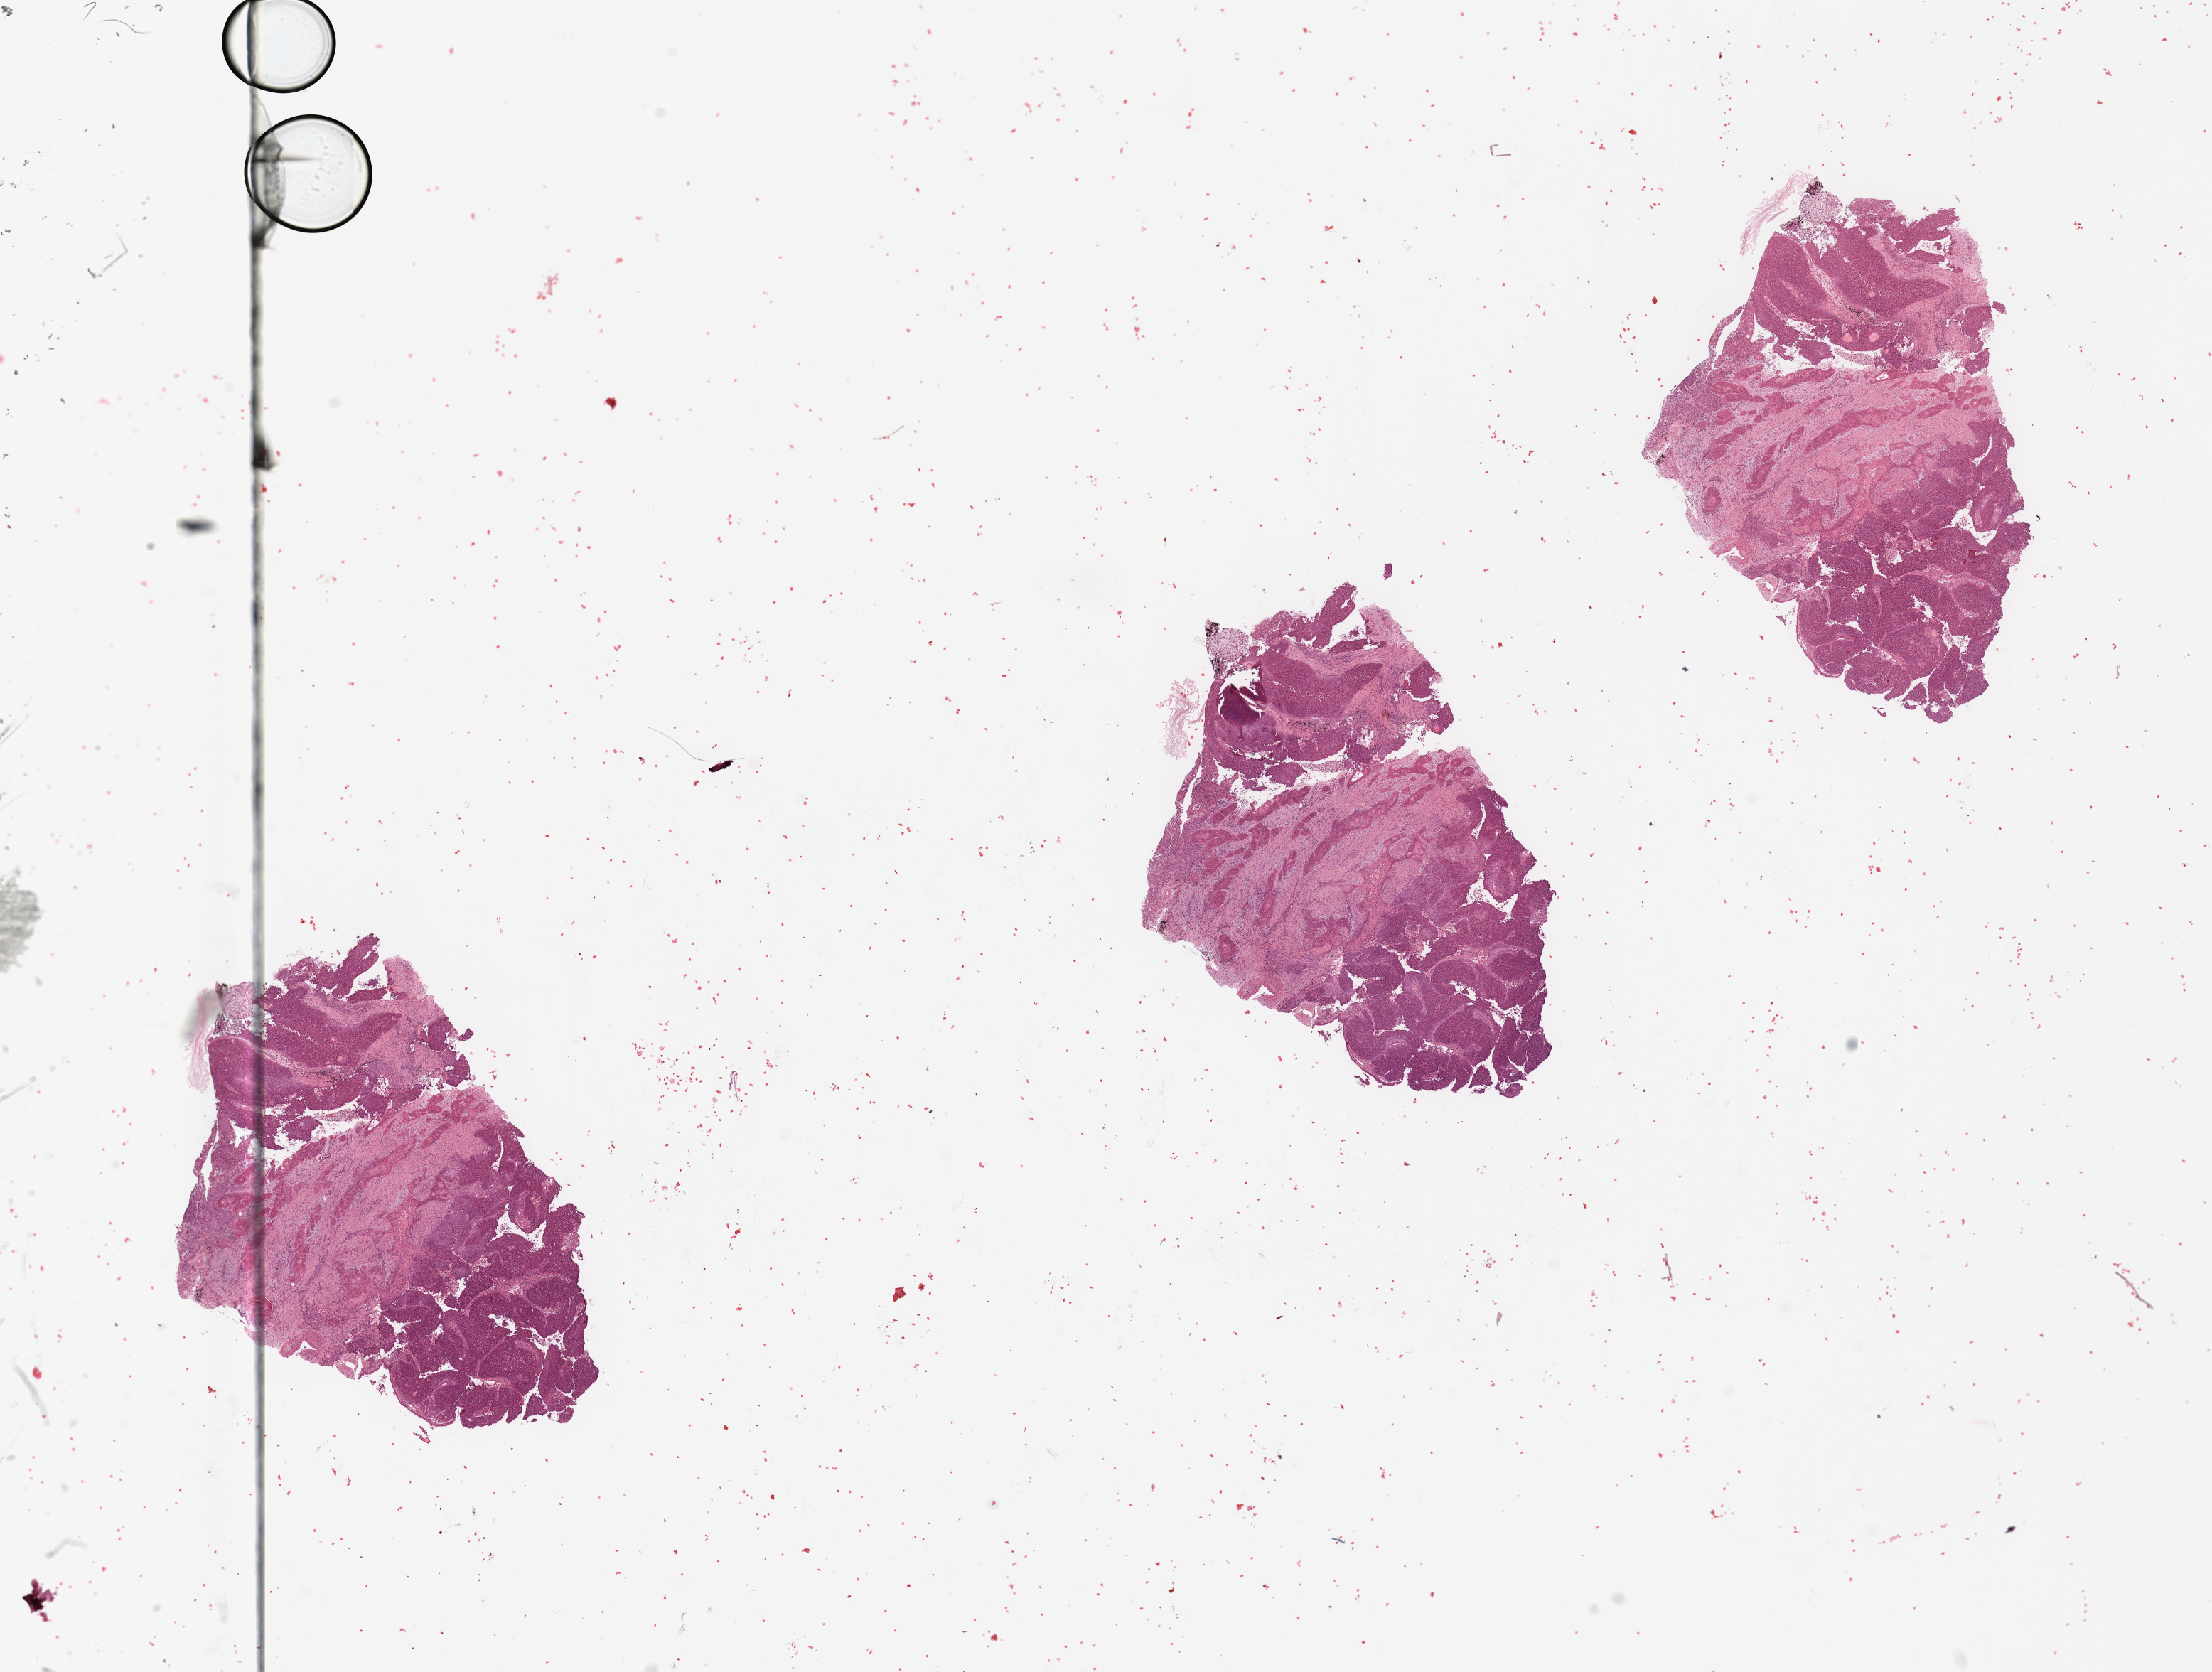
H&E whole-slide image, low-resolution overview of the scanned area, about 24.6 x 18.6 mm (slide scanned at 20x), tumour tissue sample, lung. Patient: male, age 69 years.
Diagnosis: Squamous cell carcinoma, NOS.